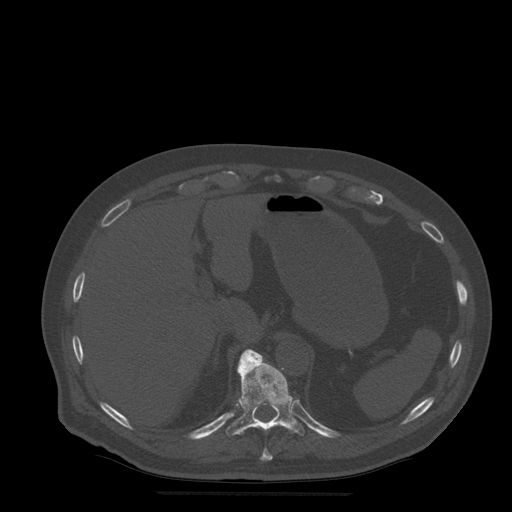
CT including the spine, one axial slice. Slice 249 of 522 in the series (ordered by position). Bone window (W 1800 / L 400 HU). 512 × 512 image matrix, field of view 420 × 420 mm. Patient age 72 years. Case-level facts recorded for this patient, not image findings: primary cancer: prostate.
Structures marked on this image (semi-automatic segmentation, software-assisted and operator-edited):
- T10 vertebra: bounding box [x1, y1, x2, y2] px = [260, 448, 273, 461]
- T11 vertebra: [226, 349, 305, 437]